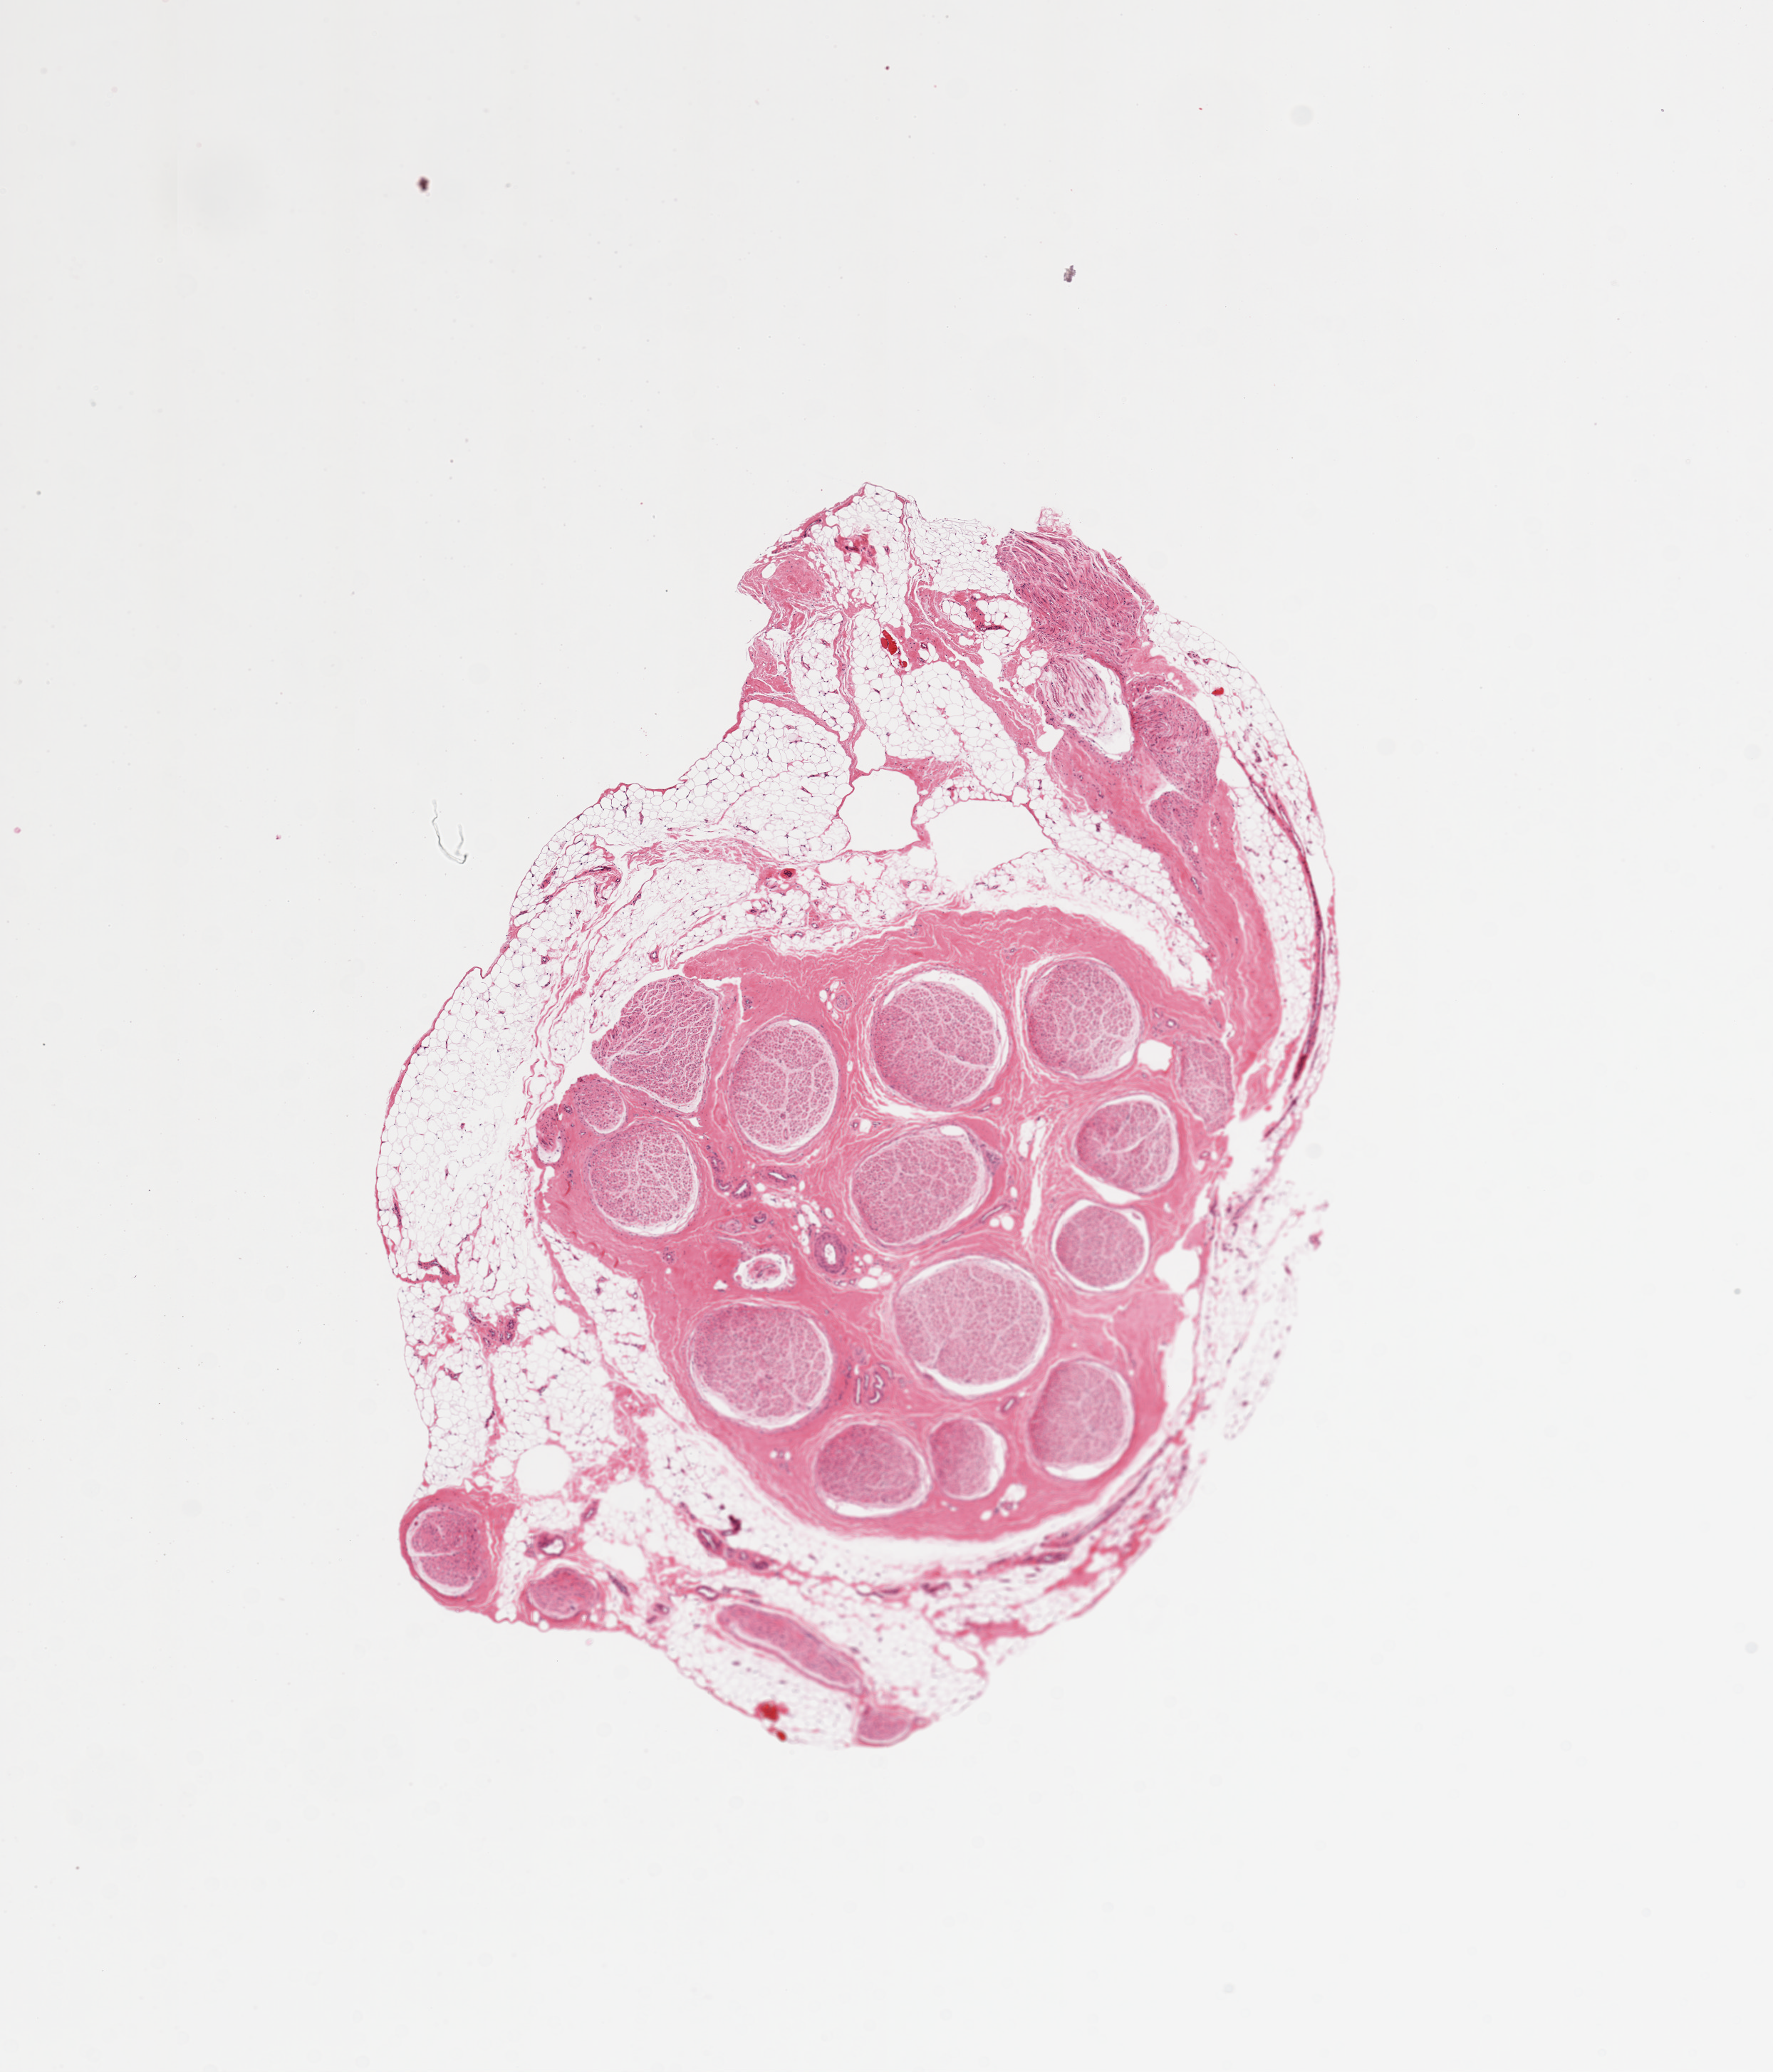
Whole-slide image, H&E stain — whole scanned area (about 9.8 x 11.5 mm) shown as a low-resolution overview, PAXgene-fixed paraffin-embedded (PFPE) section, sampled site (target tissue): tibial nerve, donor tissue sample.
Review note (as recorded): peripheral artery, not nerve. Good clean specimen. Verified mix-up. VAI to change site from Nerve to Artery.